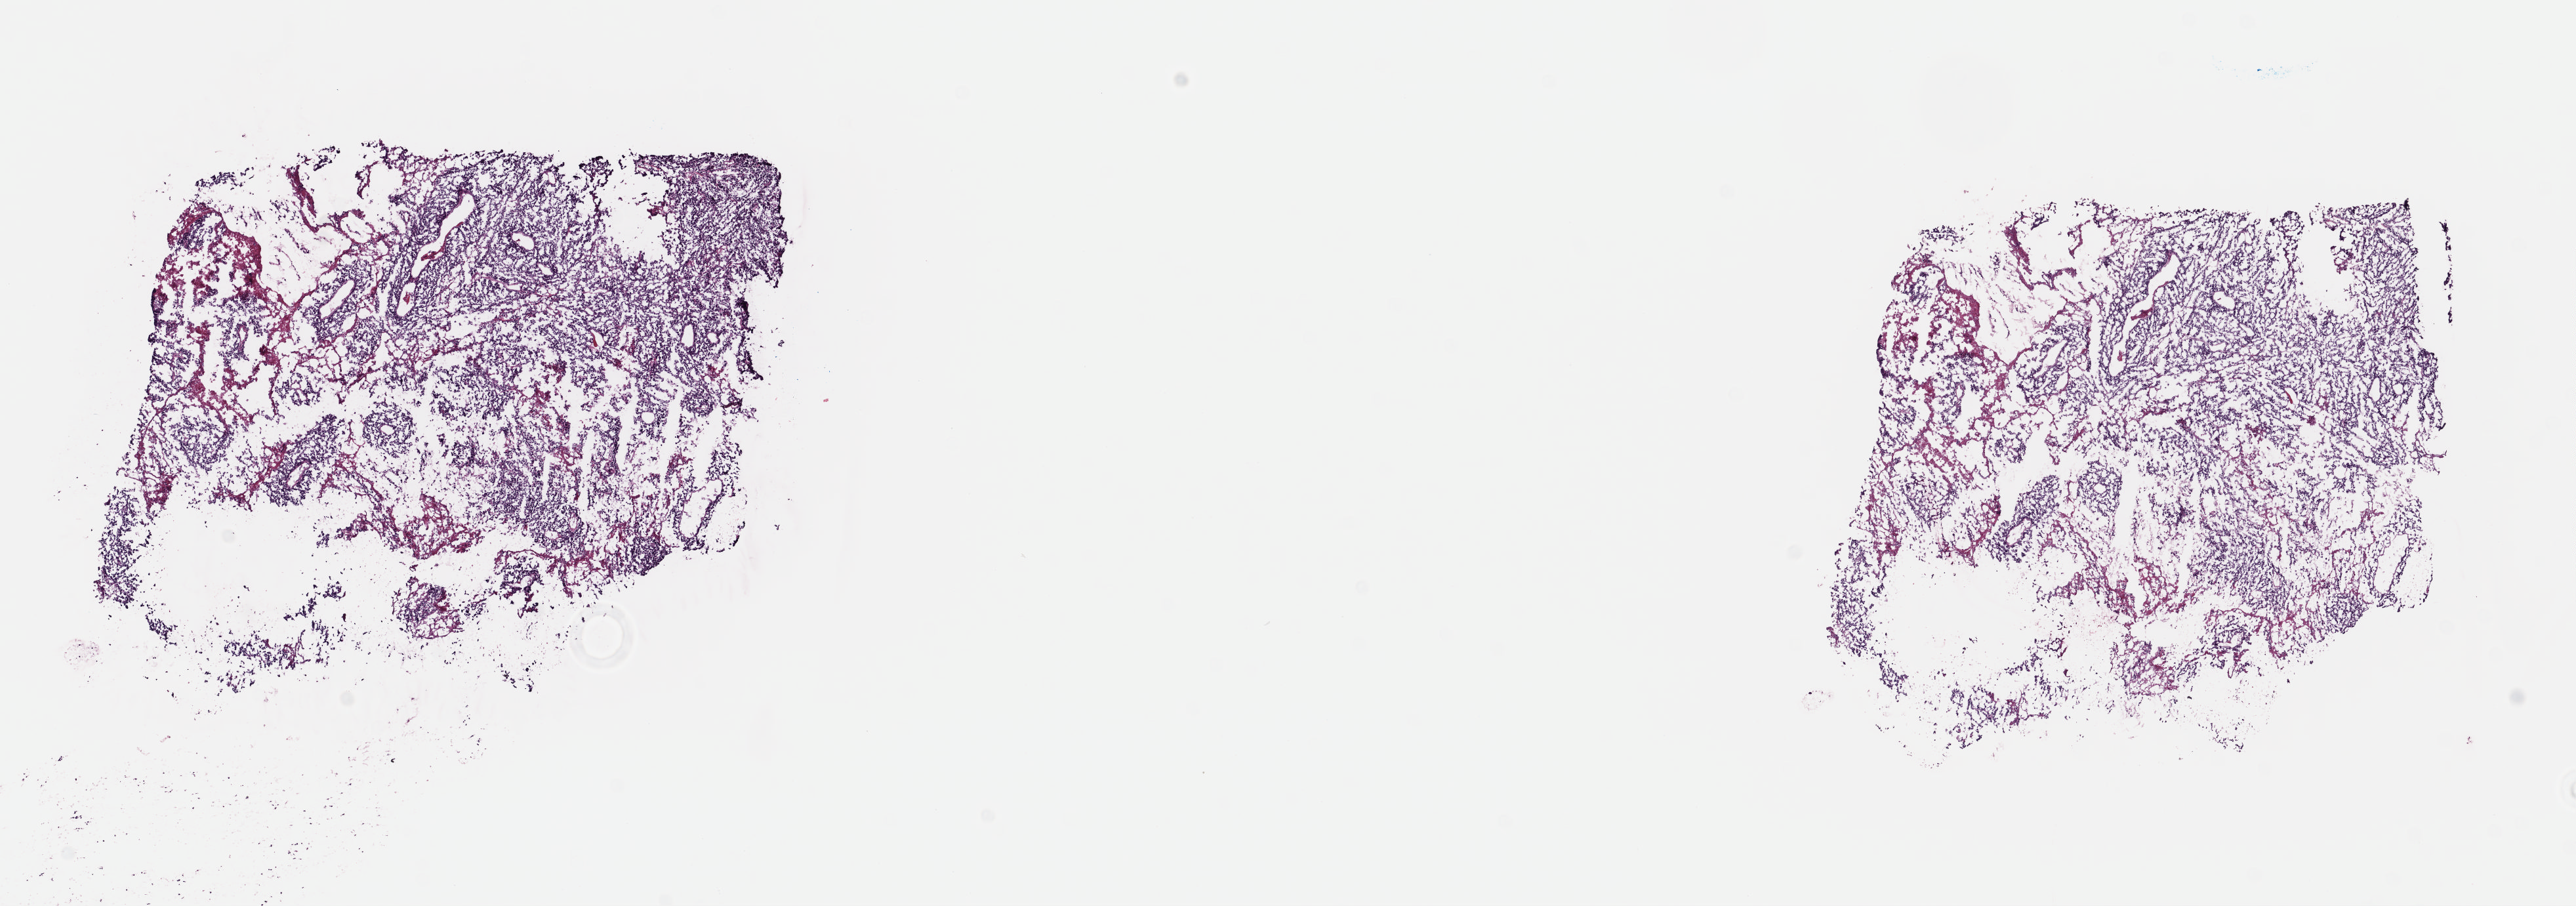
Whole-slide histology image, H&E-stained — whole scanned area (about 15.4 x 5.4 mm) shown as a low-resolution overview; frozen section from the top of the tissue portion; metastatic tumour sample, sampled site: connective, subcutaneous and other soft tissues. Male, age 39 years at initial diagnosis. Composition of this section per pathologist review: tumour cells 70%, tumour nuclei 70%, normal cells 0%, stromal cells 12%, necrosis 18%. Infiltration values recorded for this section: lymphocyte infiltration 1%, monocyte infiltration 2%, neutrophil infiltration 1%.
This section: metastatic tumour tissue. Patient diagnosis: Malignant melanoma, NOS.